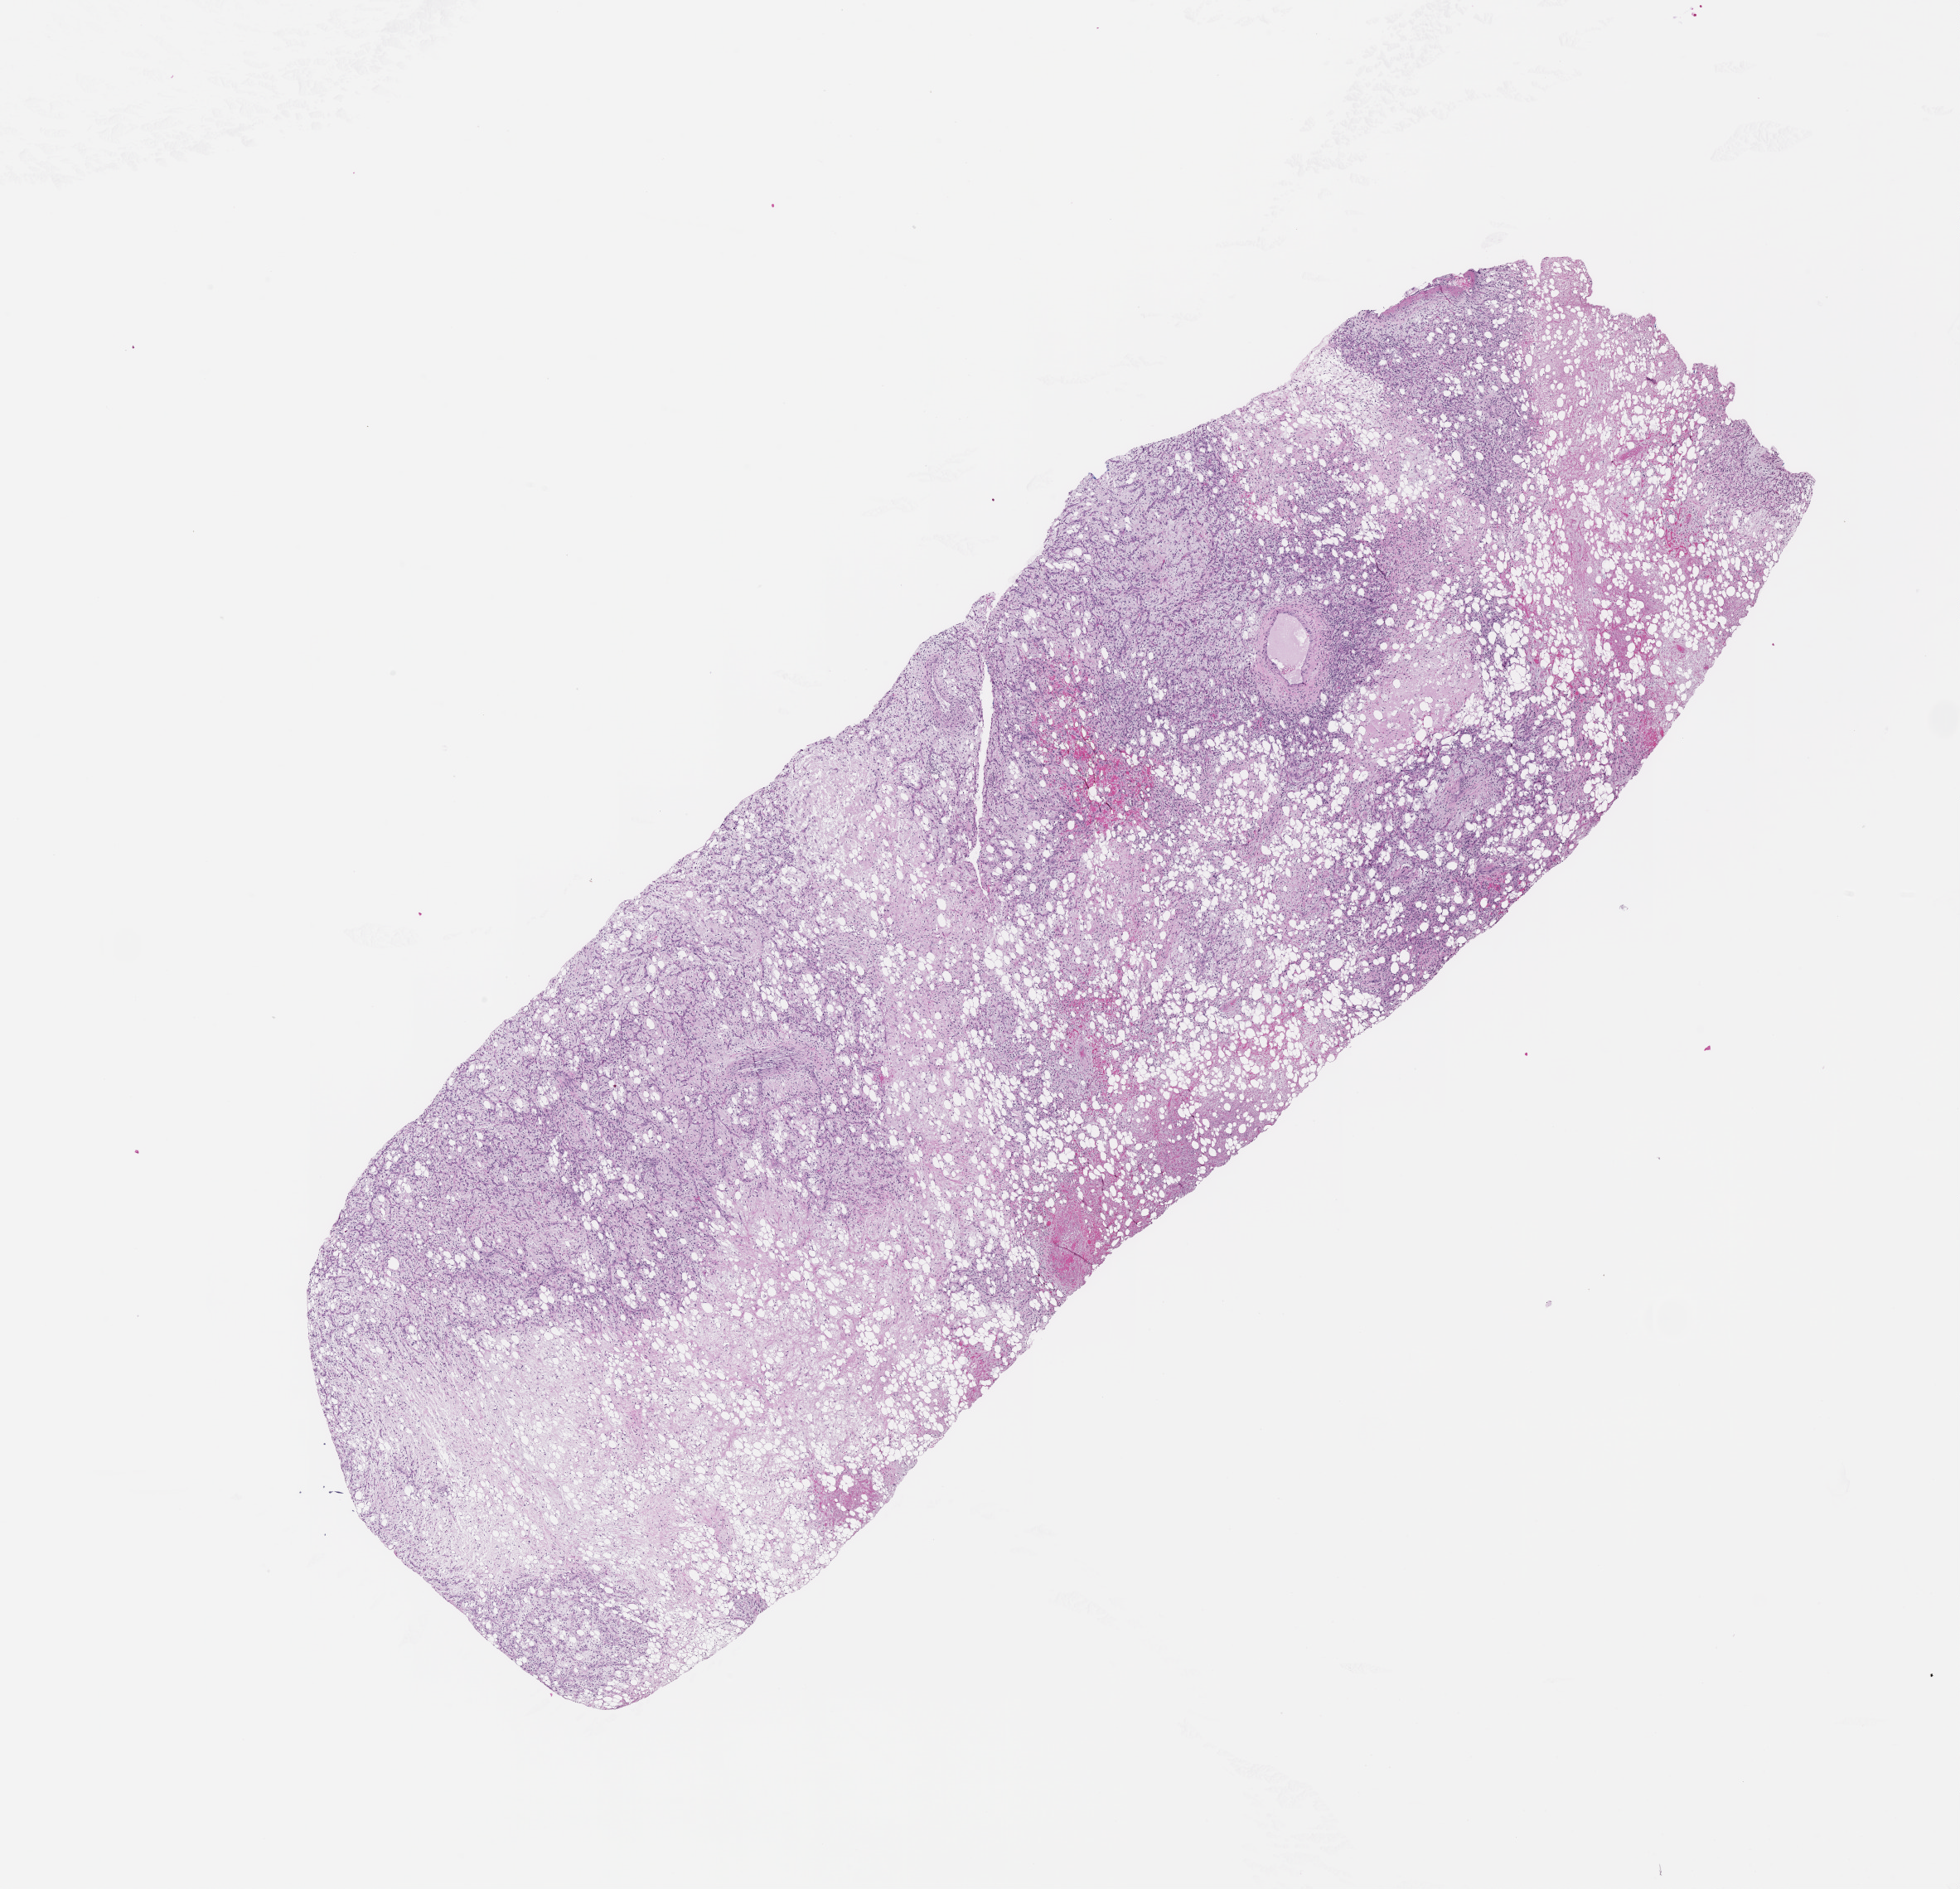
Digitized H&E-stained tissue section (whole slide), shown as a low-resolution overview of the whole scanned area (about 19.0 x 18.3 mm, slide scanned at 20x).
• patient diagnosis (cohort enrolment): sarcoma (site not recorded at cohort level)